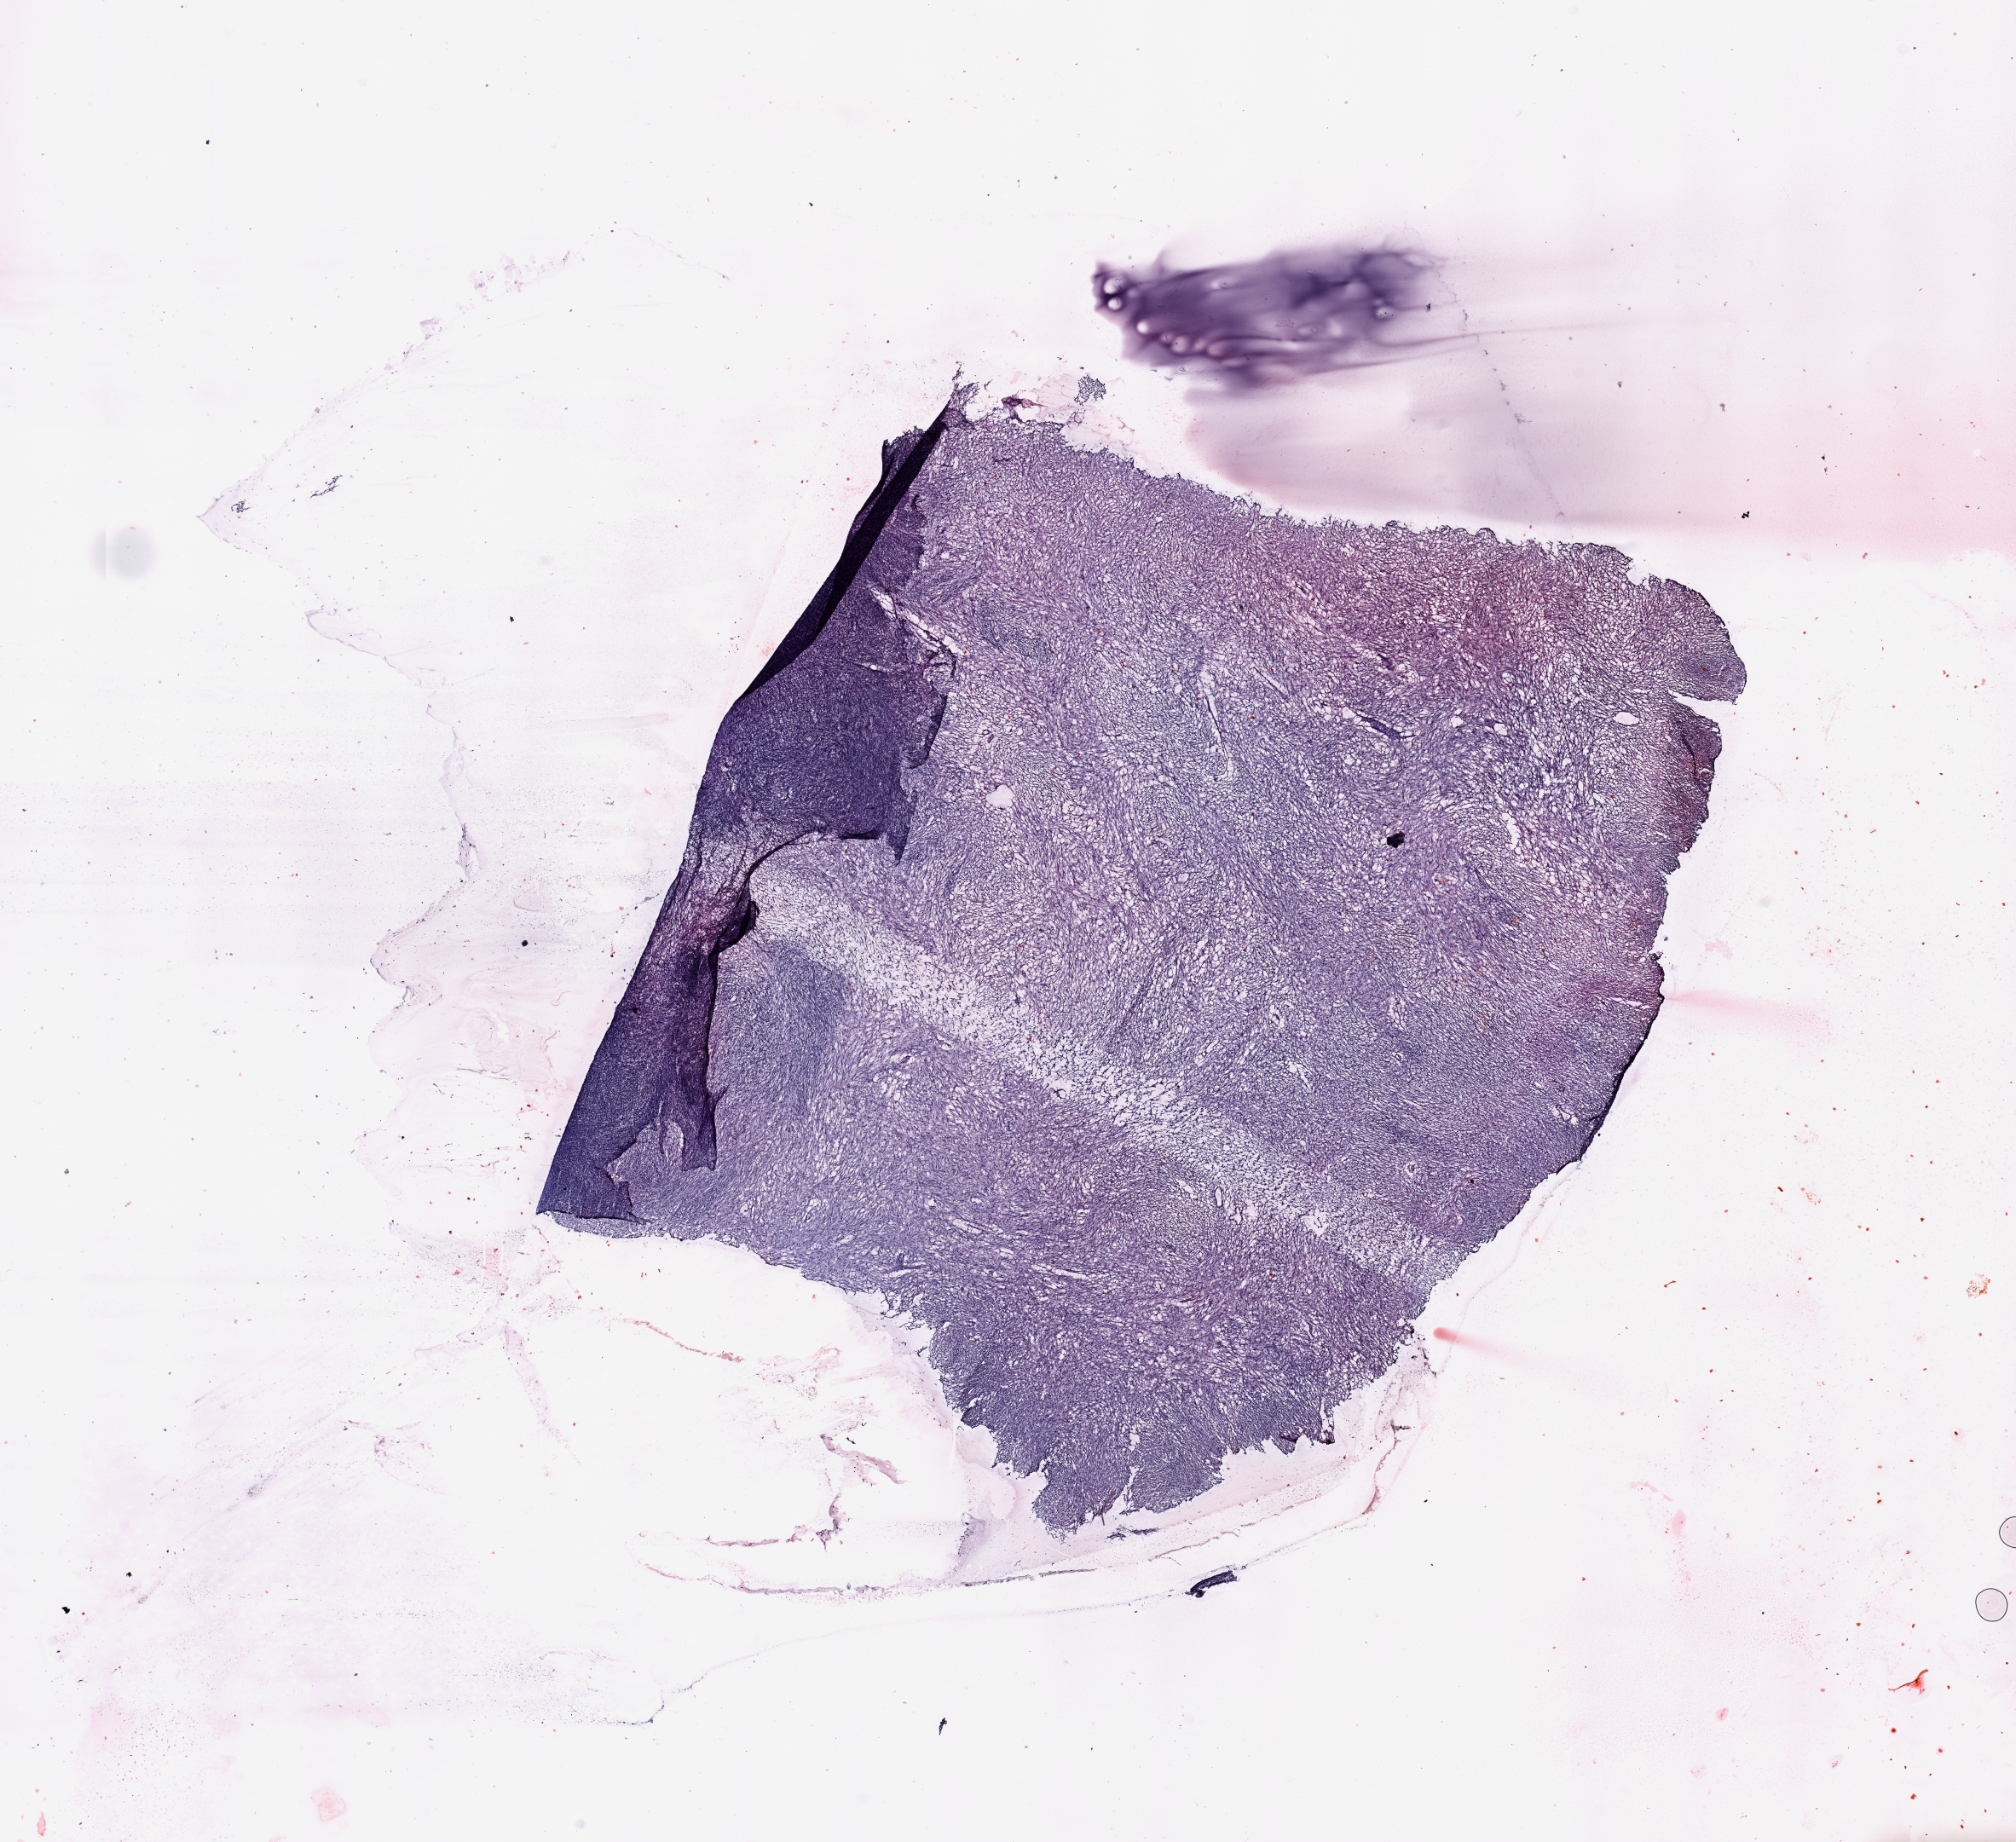
Whole-slide histology image, H&E-stained — low-resolution overview of the scanned area, about 18.7 x 17.1 mm. Female, 65 y/o.
Patient diagnosis (cohort enrolment): sarcoma (site not recorded at cohort level). Primary tumour site (as recorded): gynecologic.